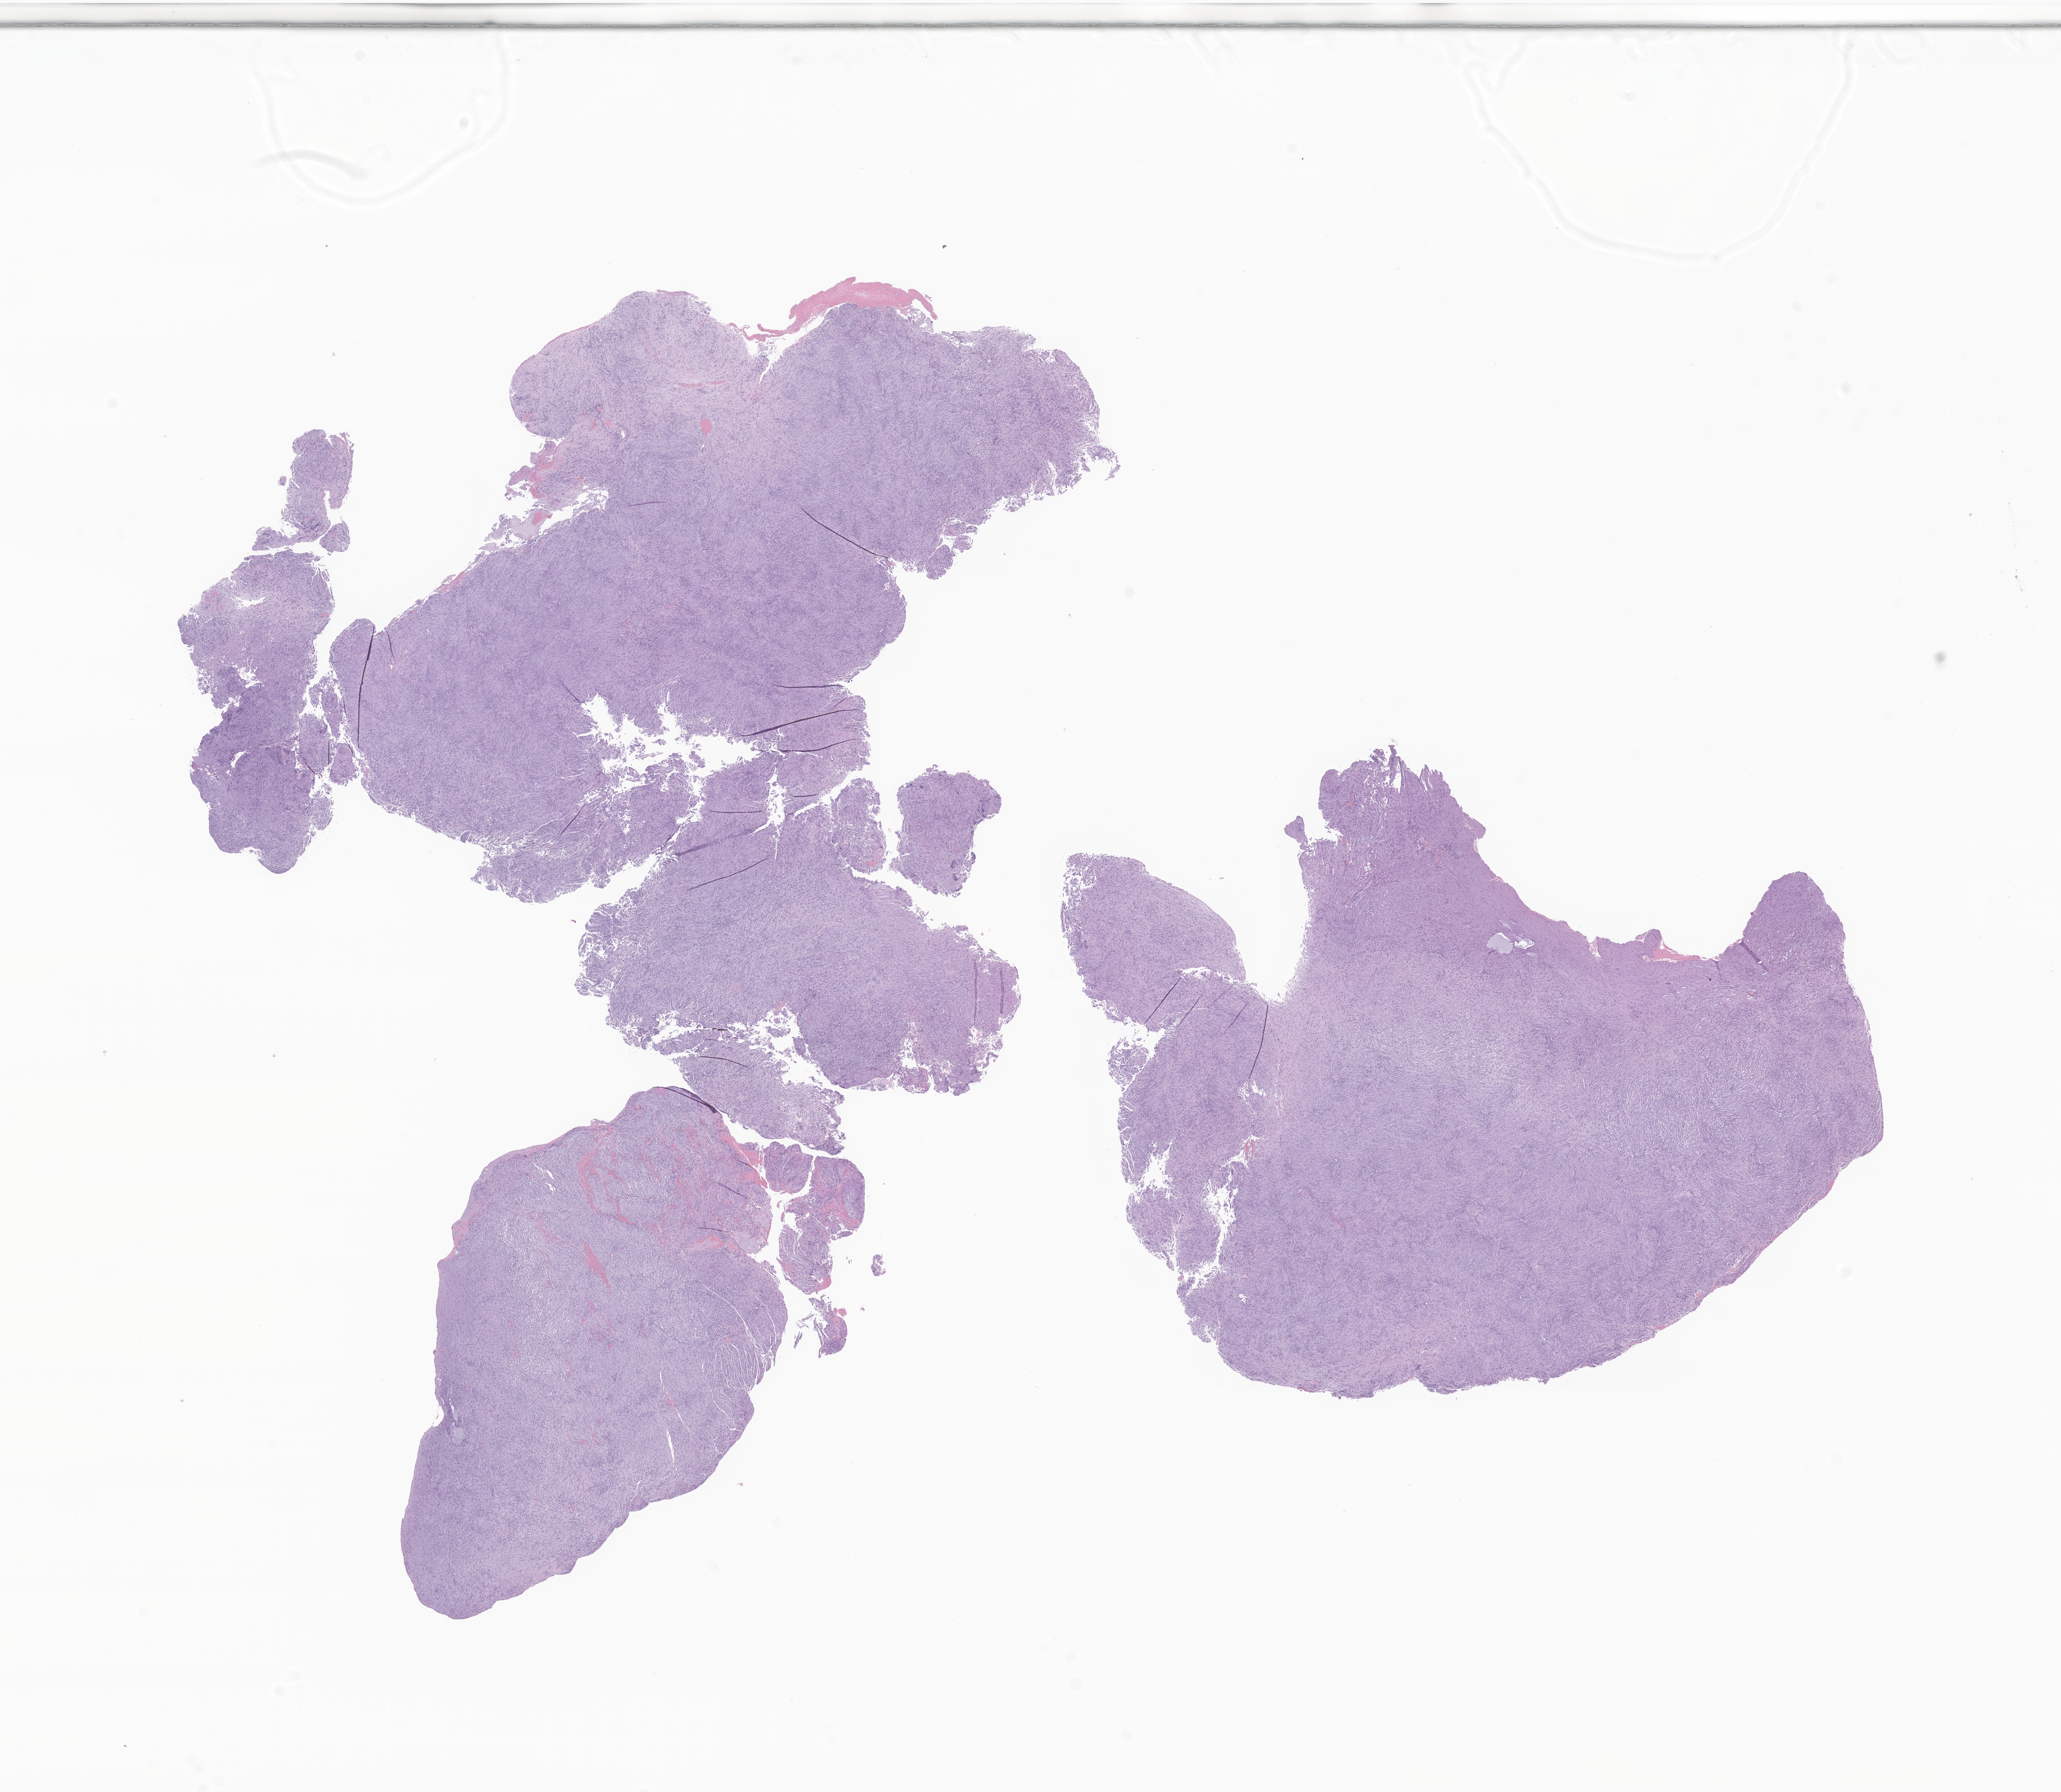
Hematoxylin and eosin (H&E) whole-slide image of tumor tissue from the parietal lobe — low-resolution overview of the scanned area, about 21.6 x 18.8 mm. Formalin-fixed, paraffin-embedded (FFPE) tissue. Male patient, age 163 months (13 years 7 months).
Recorded diagnosis: Neoplasm, uncertain whether benign or malignant.